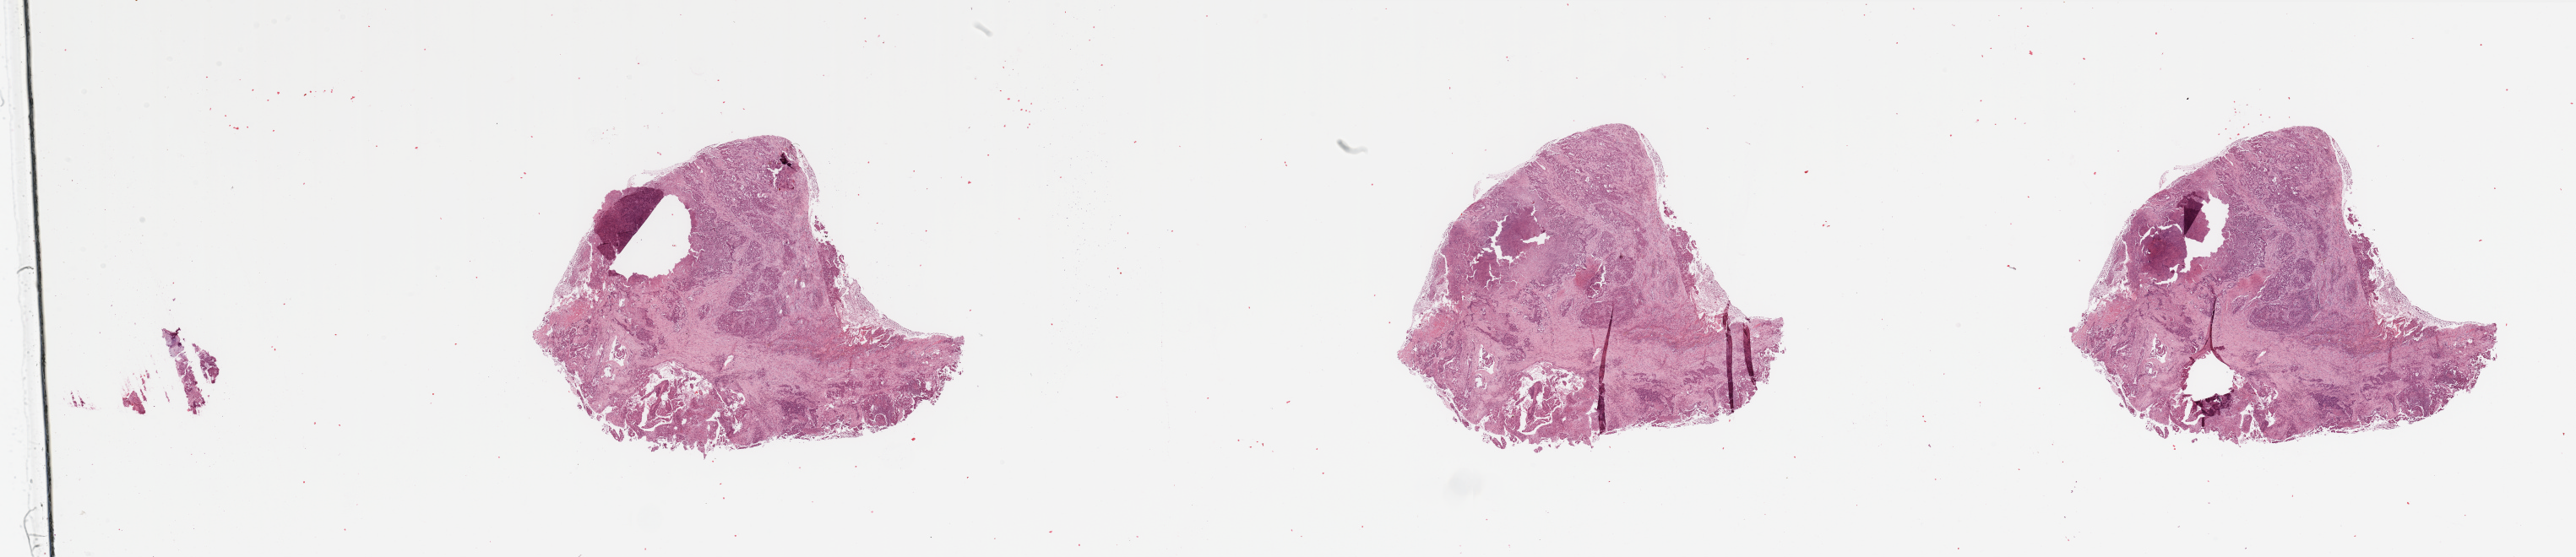
H&E-stained whole-slide image, low-resolution overview of the scanned area, about 48.2 x 10.4 mm (from a 20x scan). Lung, tissue type not recorded.
* patient diagnosis (cohort enrolment): lung adenocarcinoma (lung)